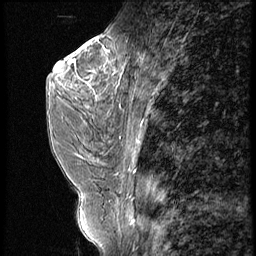
Breast MRI (dynamic contrast-enhanced), one sagittal slice; slice 28 of 56 in the series (ordered by position); 4 images stored at this slice position (order not interpretable as contrast timing); 1.5 T; TE 4.2 ms, TR 9 ms; 256 × 256 image matrix, field of view 180 × 180 mm. Patient: female, 44 years. From the clinical record (not read from this slice): setting: breast cancer imaged before/during neoadjuvant chemotherapy; receptor status: triple-negative.
Annotated regions visible in this slice (semi-automatic segmentation, software-assisted and operator-edited):
- analysis volume of interest (the breast-tissue region the enhancement analysis was run in; not a lesion): box from (x=87, y=28) to (x=132, y=99) px
- tumour enhancement mask (voxels above the 140 % enhancement threshold inside the analysis volume of interest): (x=87, y=48)–(x=124, y=84)